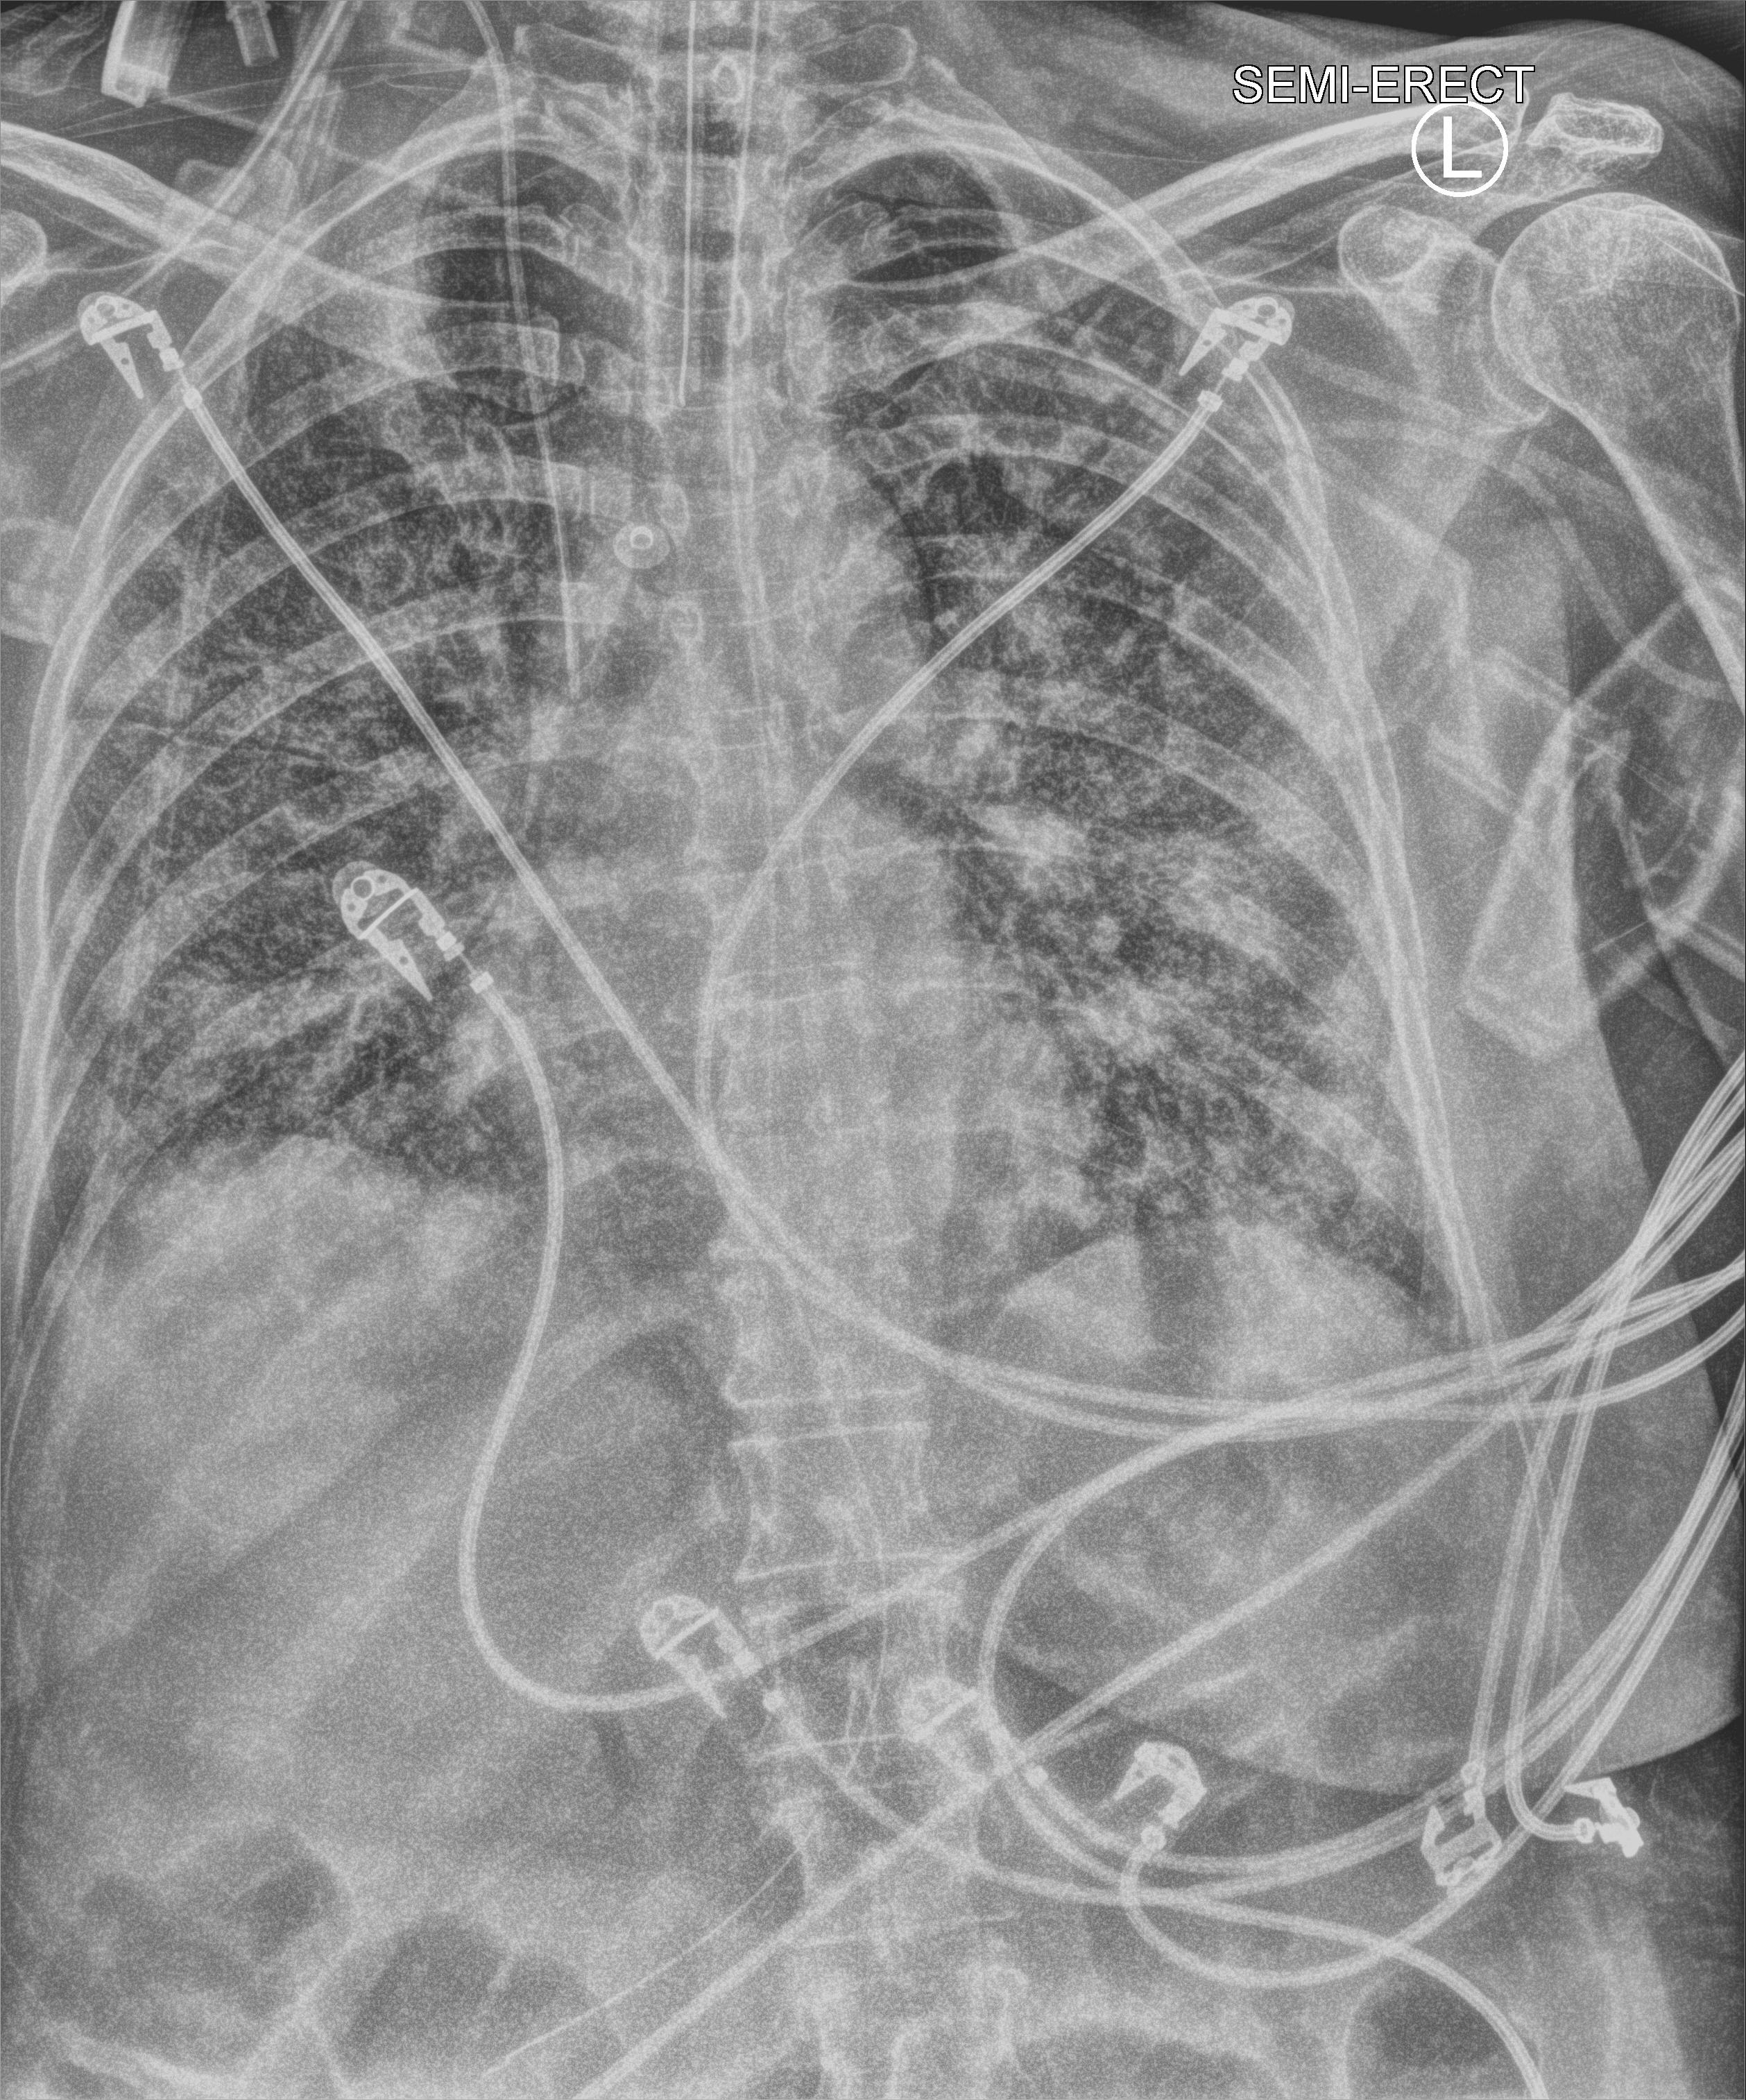
Chest X-ray (portable); anteroposterior (AP) projection. Female patient hospitalised with COVID-19, age 60–74 years.
From the hospital-stay record, not from the radiograph (when in the stay this image was taken is not recorded):
- length of hospital stay: 43 days